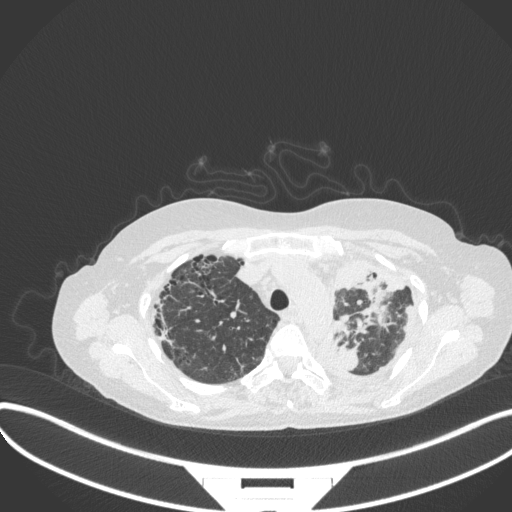
Chest CT, one axial slice; position 265 of 373 along the scan axis; reconstruction kernel B31f; 120 kVp; lung window (W 1500 / L -600 HU); 512 × 512 image matrix, field of view 400 × 400 mm. Female patient, age 56 years. From the clinical record (not read from this slice): clinical TNM (as recorded): T1 N0 M0.
Annotated regions visible in this slice (rectangle marked by the reading radiologist):
- lung tumour (recorded histology: adenocarcinoma): box from (x=343, y=256) to (x=404, y=328) px